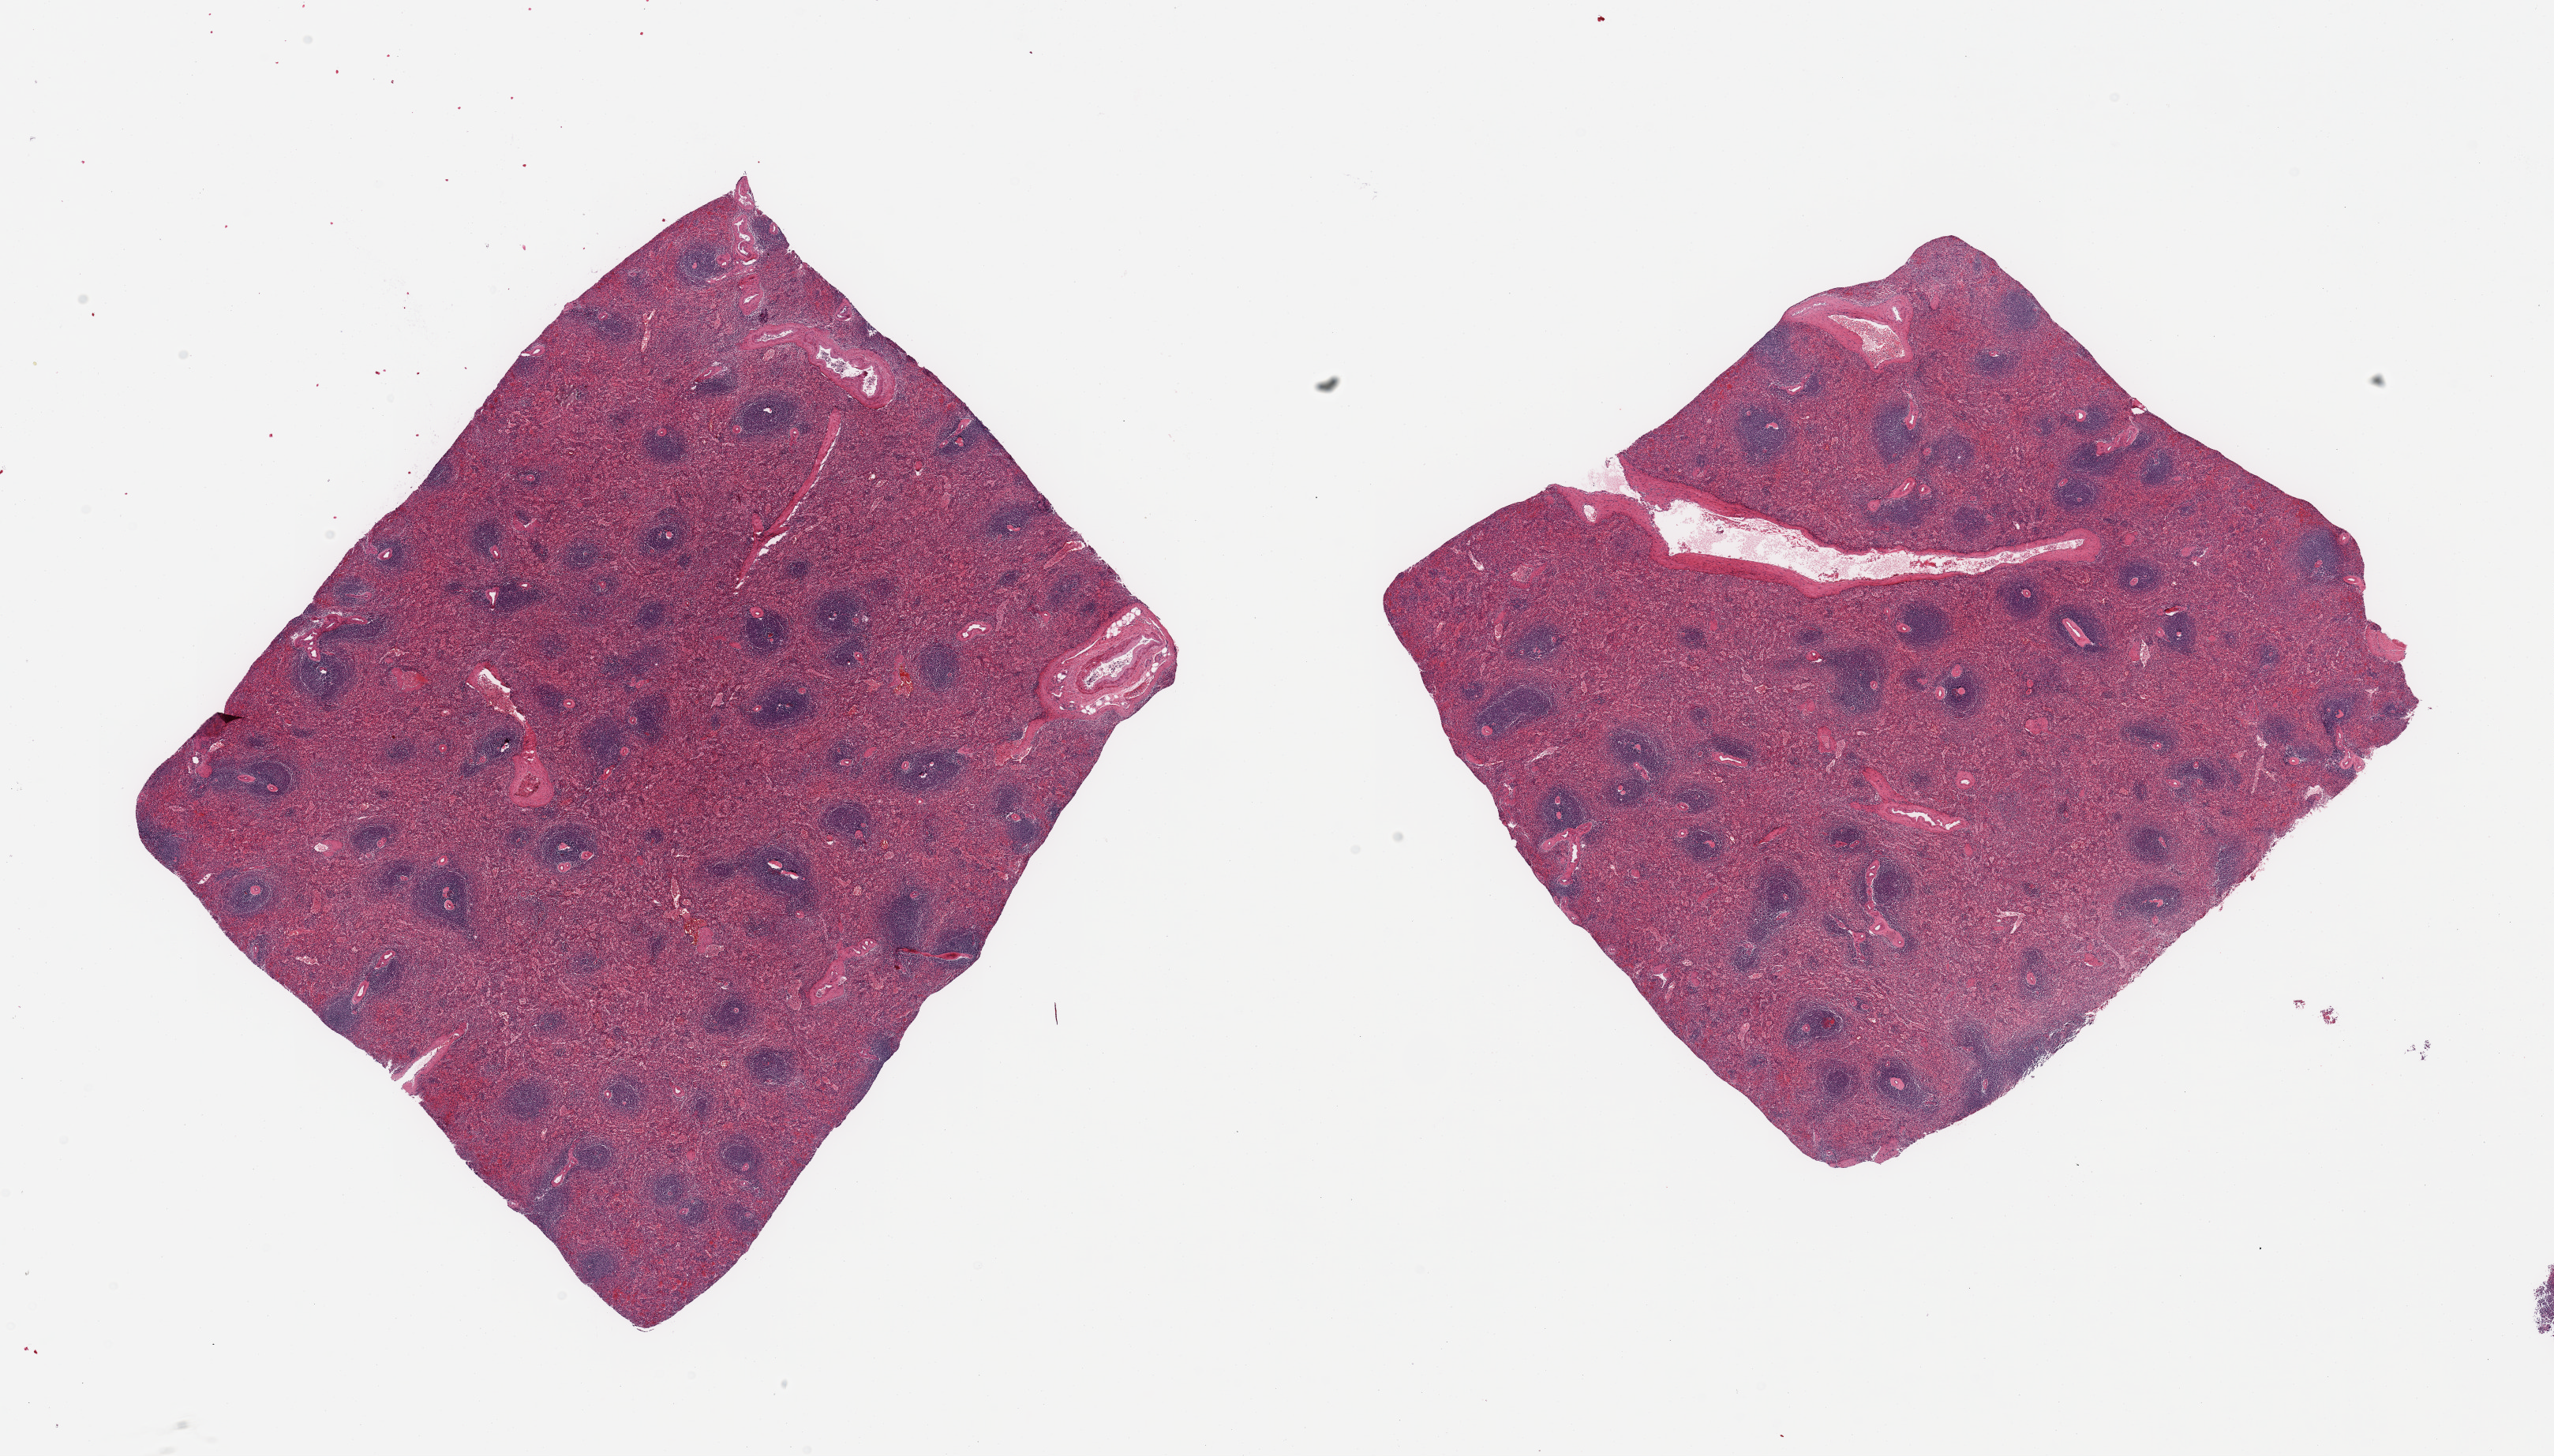
Digitized H&E-stained section, shown as a low-resolution overview of the whole scanned area (about 25.6 x 14.6 mm). PAXgene-fixed paraffin-embedded (PFPE) section. Section of spleen (target tissue). Donor tissue sample. Female donor.
Pathologist's review note for this sample: 2 pieces; spleen, not liver; congestion.